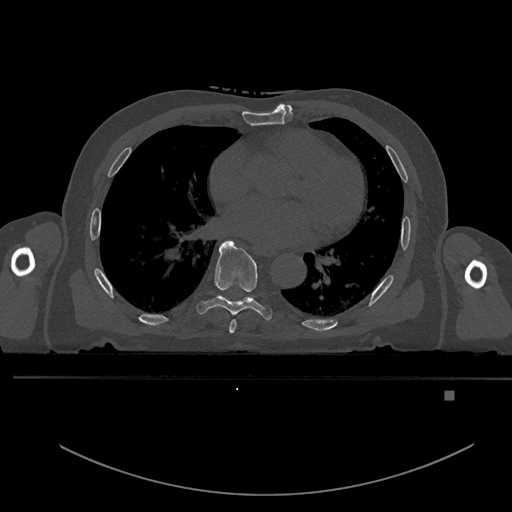
CT including the spine, one axial slice; slice 254 of 969 in the series (ordered by position); bone window (W 1800 / L 400 HU); 512 × 512 image matrix. Male patient, age 82 years. Case-level facts recorded for this patient, not image findings: primary cancer: prostate; vertebrae with lytic lesions (as recorded): T11, T9, T8, T2.
Structures marked on this image (semi-automatic segmentation, software-assisted and operator-edited):
- T6 vertebra: box from (x=229, y=319) to (x=237, y=334) px
- T7 vertebra: (x=196, y=240)–(x=273, y=320)
- T8 vertebra: (x=221, y=295)–(x=255, y=301)